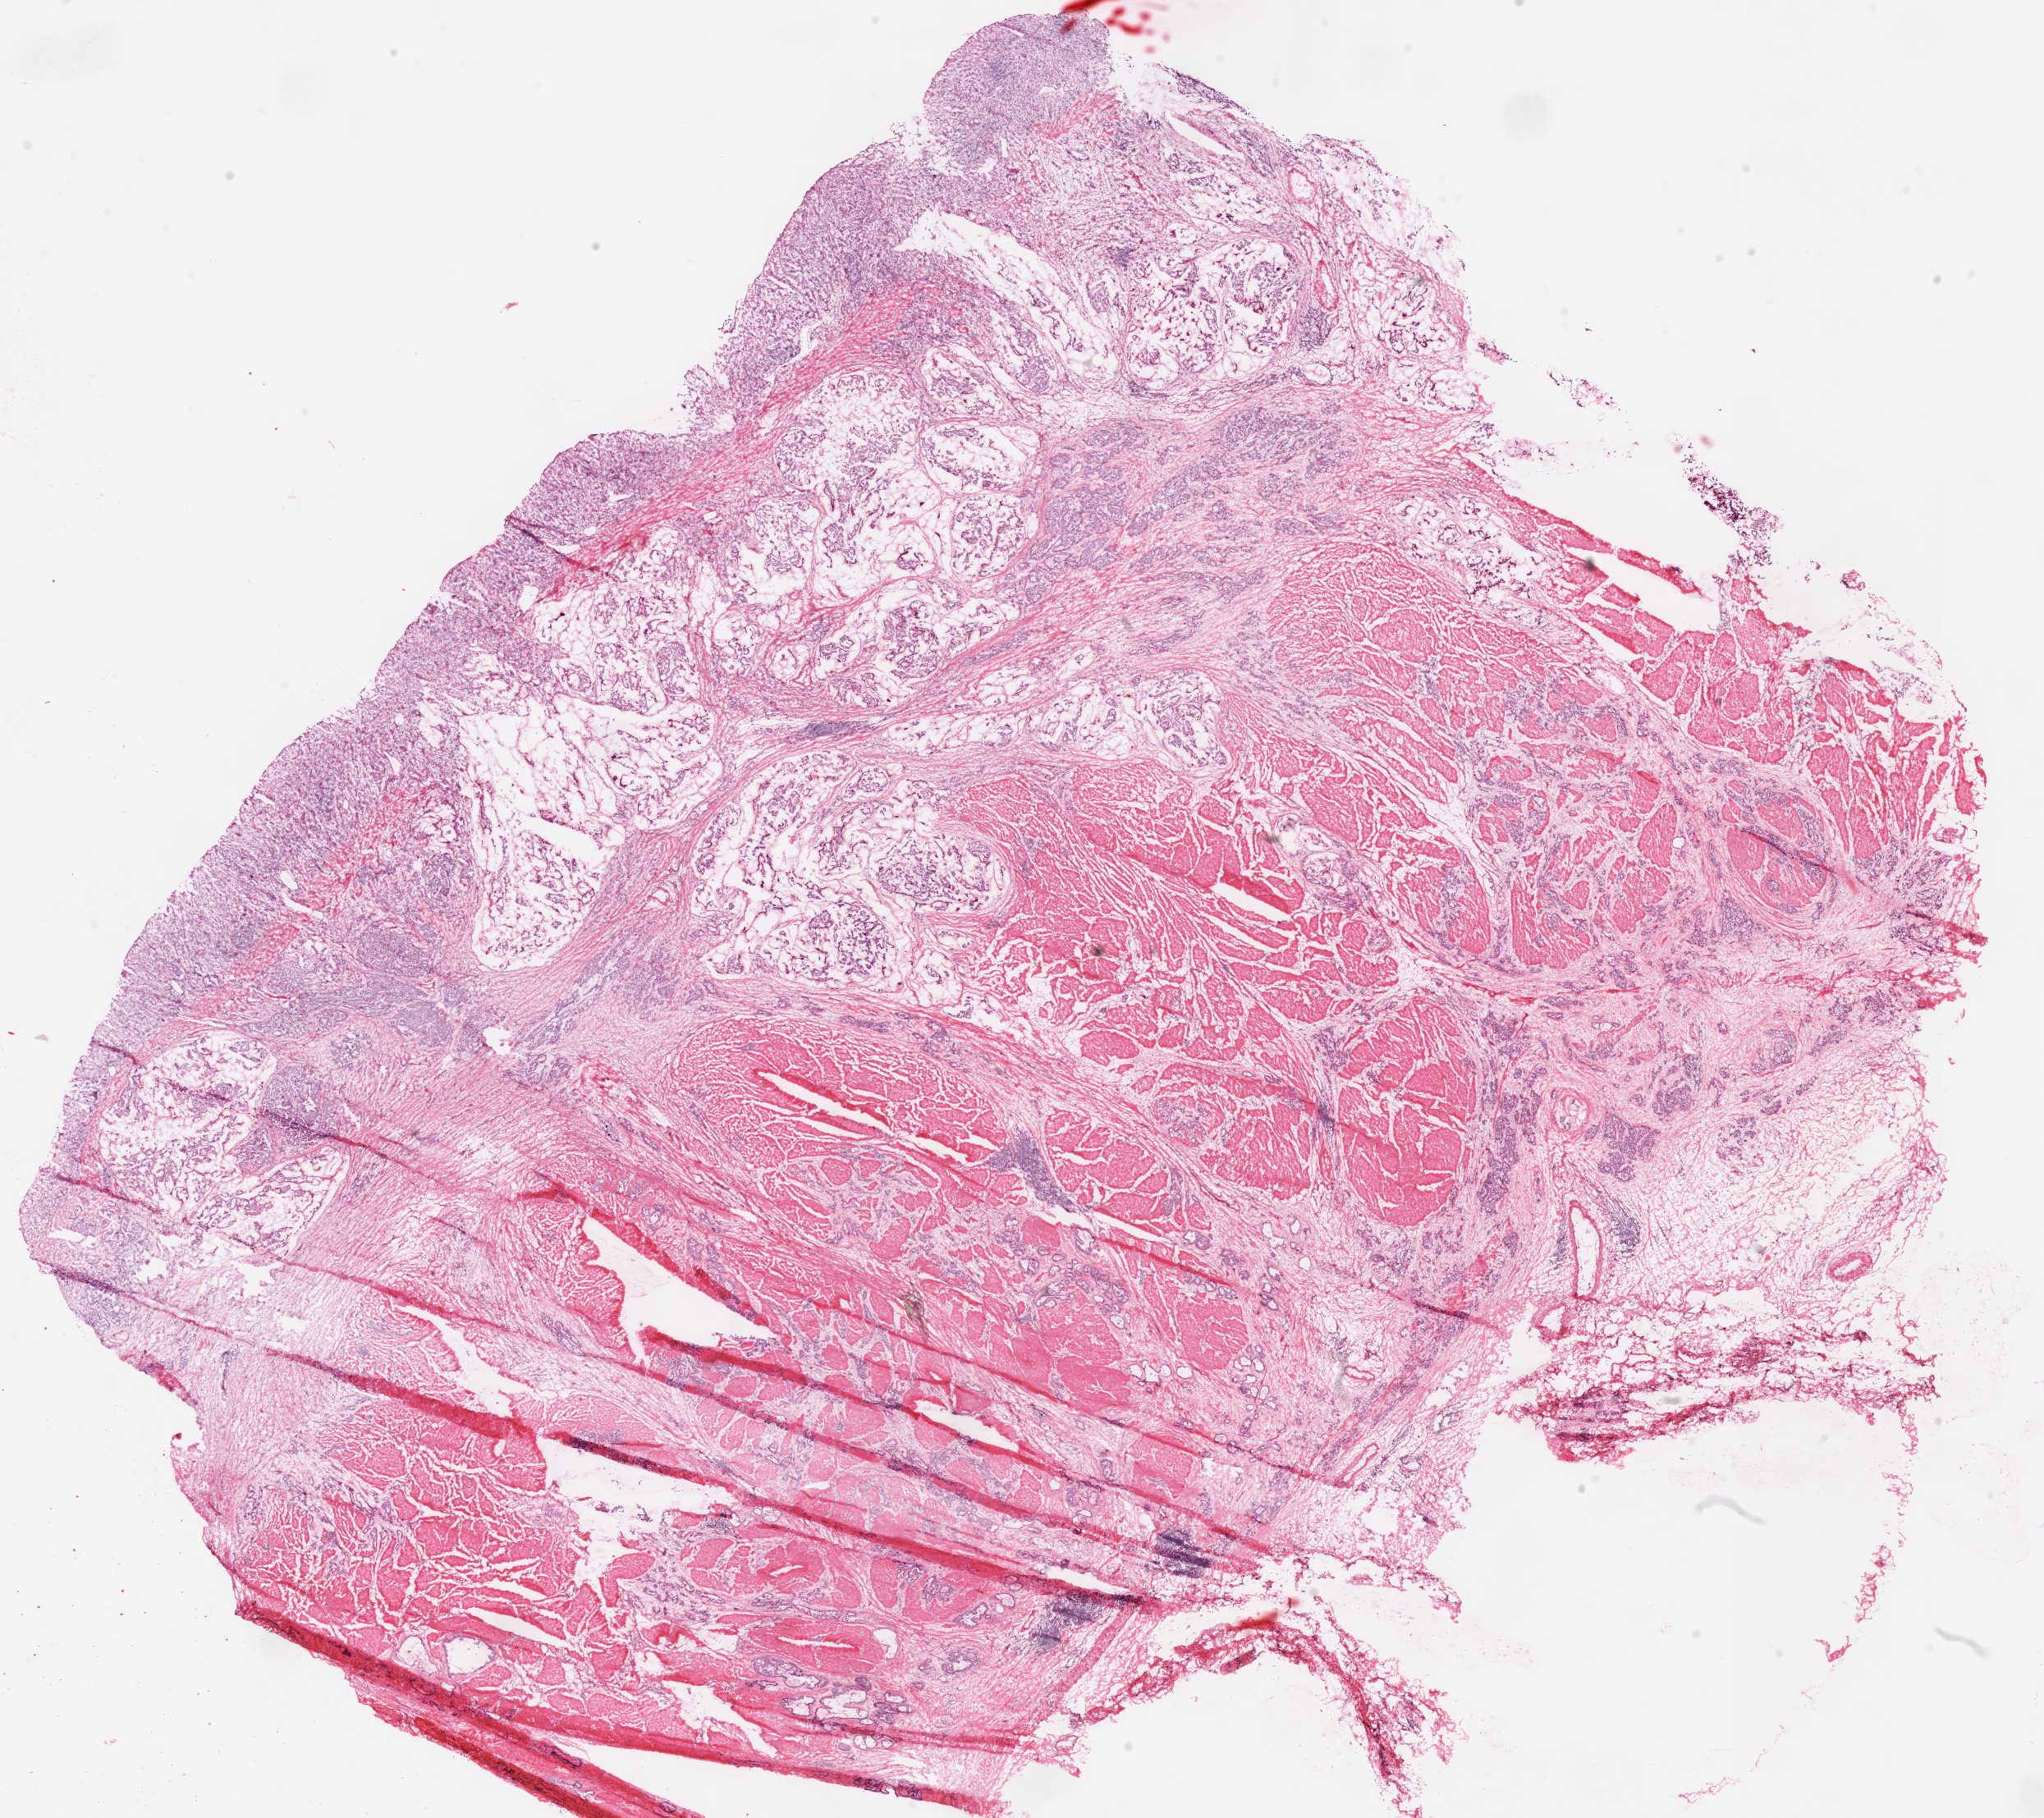
Whole-slide histology image, H&E — a low-resolution overview of the entire scanned area, about 19.6 x 17.4 mm (acquisition: 40x scan), frozen section from the top of the tissue portion, primary tumour sample from the stomach. Female patient; age at initial diagnosis 76 years. Histologic grade: G3 (poorly differentiated). Composition of this section per pathologist review: tumour cells 75%, tumour nuclei 75%, normal cells 0%, stromal cells 25%, necrosis 0%.
* histologic diagnosis: Adenocarcinoma, NOS (fundus of stomach)
* AJCC pathologic stage: IIIB (7th edition)
* TNM: T3 N3a M0
* lymph nodes positive (case pathology): 7 of 15 examined